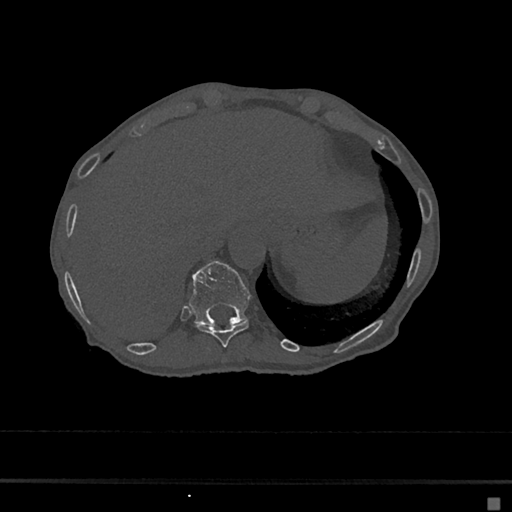
CT including the spine, one axial slice; slice 201 of 797 in the series (ordered by position); reconstruction kernel Br40s/3; 120 kVp; bone window (W 1800 / L 400 HU); 0.5 mm slice thickness; 512 × 512 image matrix, field of view 360 × 360 mm. Patient: female, 68 years. Case-level facts recorded for this patient, not image findings: primary cancer: renal.
Outlined on this slice (semi-automatically segmented with operator editing):
- T10 vertebra: bounding box <196,320,249,347> (left, top, right, bottom; pixels)
- T11 vertebra: <189,261,252,325>